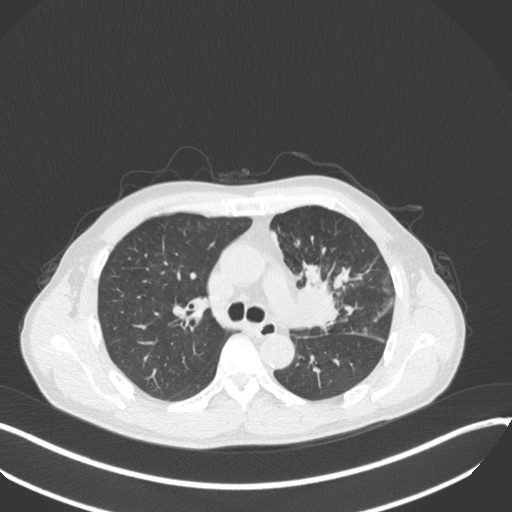
Chest CT, one axial slice. Reconstruction kernel B31f. 120 kVp. Lung window (W 1500 / L -600 HU). 1 mm slice thickness. 512 × 512 image matrix. Male patient, age 56 years. From the clinical record (not read from this slice): clinical TNM (as recorded): T2a N0 M0.
Outlined on this slice (rectangle marked by the reading radiologist):
- lung tumour (recorded histology: squamous cell carcinoma): bounding box (x1, y1, x2, y2) in pixels: (292, 260, 342, 336)